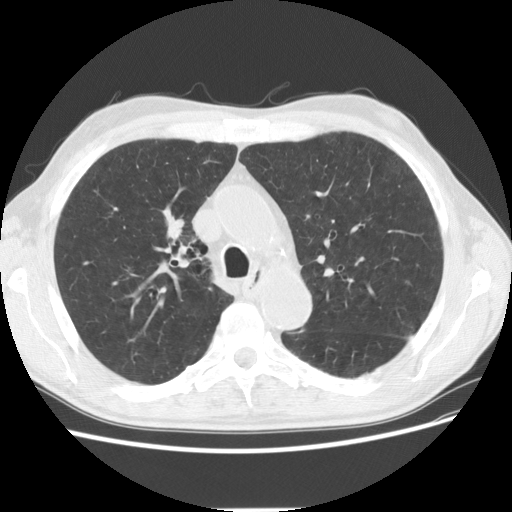
Chest CT (low-dose screening protocol), one axial image. First (baseline) screen. Lung window (W 1500 / L -600 HU). 2.5 mm slice thickness. Slice 44 of 135 in the series. Male, age 73 years at enrolment.
• Lesion marked by an expert reader, box from (x=141, y=196) to (x=206, y=260) px.
• Screening reader's record for this exam (one nodule recorded; not confirmed to be the boxed lesion): non-calcified nodule or mass ≥4 mm, right upper lobe, 16 × 9 mm, spiculated (stellate) margins, soft tissue attenuation.